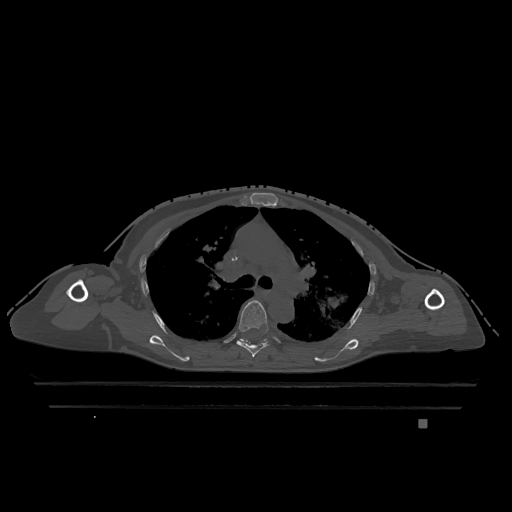
CT including the spine, one axial slice. Slice 828 of 1317 in the series (ordered by position). Bone window (W 1800 / L 400 HU). 0.5 mm slice thickness. 512 × 512 image matrix, field of view 500 × 500 mm. Female patient, age 74 years. From the clinical record (not read from this slice): primary cancer: lung.
Outlined on this slice (semi-automatic segmentation, software-assisted and operator-edited):
- T5 vertebra: bounding box [x1, y1, x2, y2] px = [237, 300, 269, 357]
- T6 vertebra: [239, 338, 267, 344]